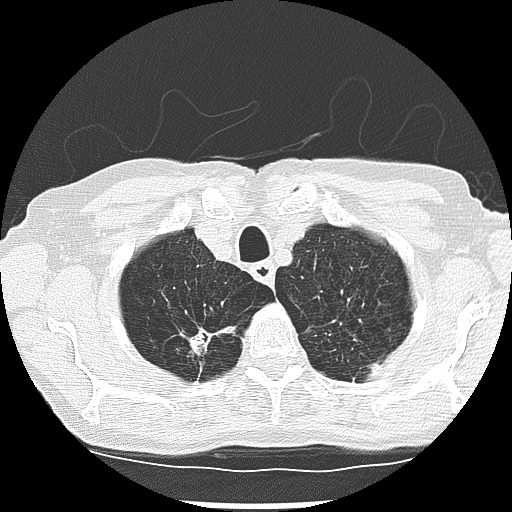
Low-dose screening chest CT, one axial slice; position 235 of 265 along the scan axis; lung window (W 1500 / L -600 HU); 2.5 mm slice thickness; 512 × 512 image matrix, field of view 300 × 300 mm.
Outlined on this slice (expert manual segmentation):
- lesion 2 (tumor, upper lobe of right lung): bounding box <188,329,214,354> (left, top, right, bottom; pixels)